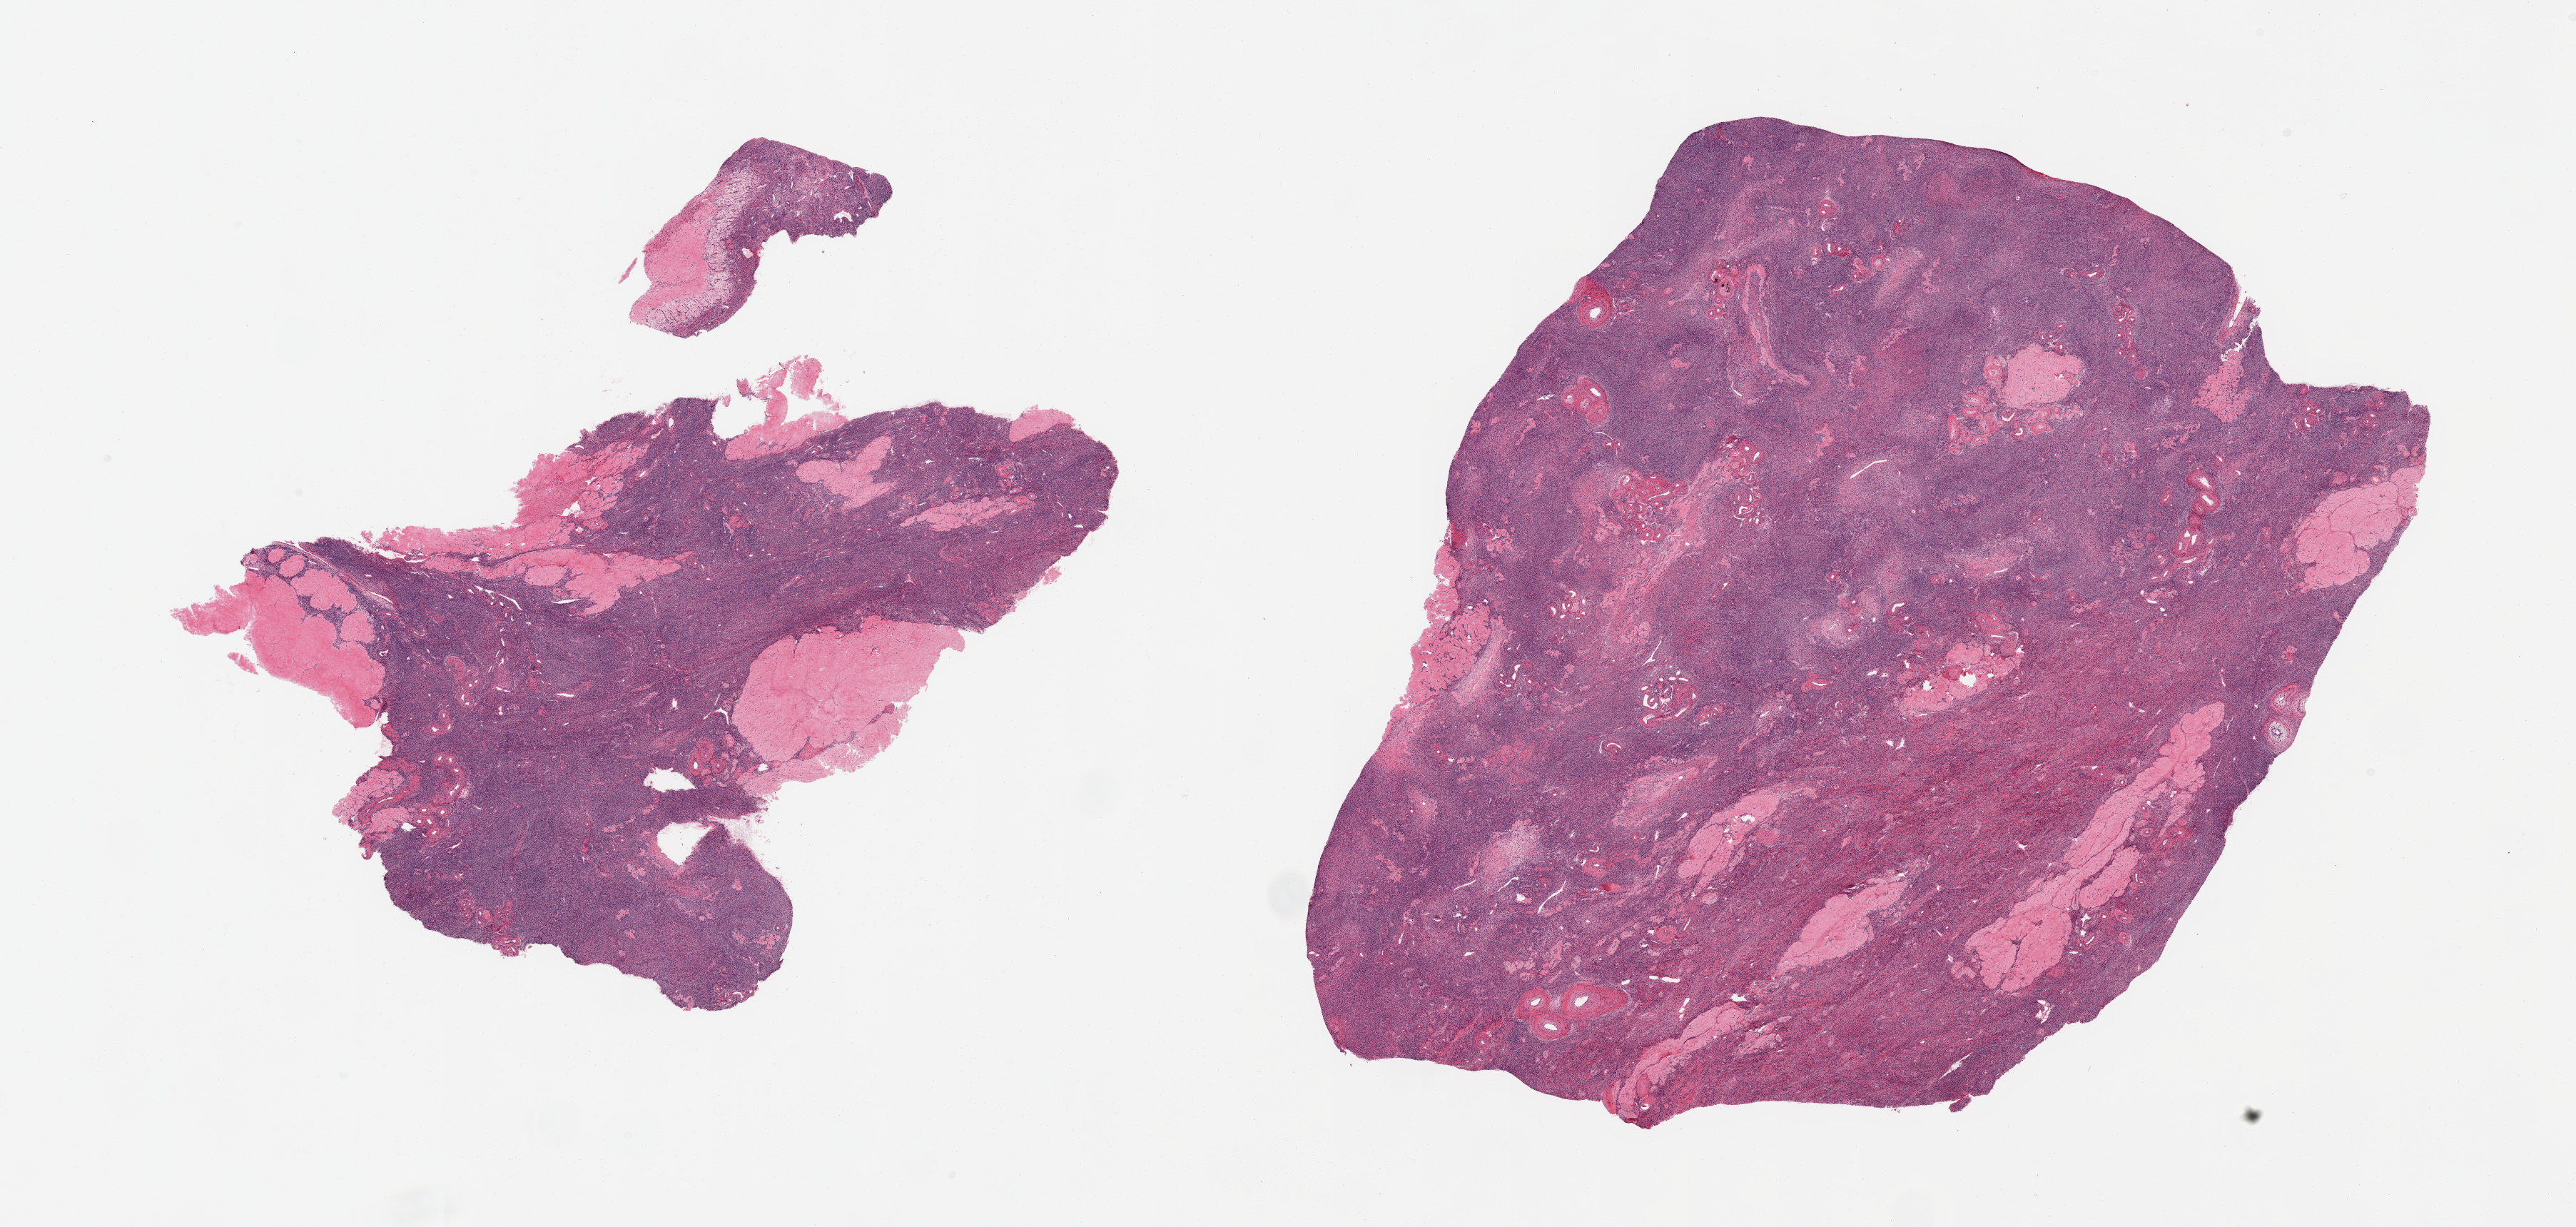
Whole-slide image, hematoxylin and eosin (H&E) stain, a low-resolution overview of the entire scanned area, about 28.5 x 13.6 mm (slide scanned at 20x). PAXgene-fixed, paraffin-embedded tissue. Sampled site (target tissue): ovary. Tissue donor sample.
• review note (as recorded): 2 pieces, post menopausal involutional changes